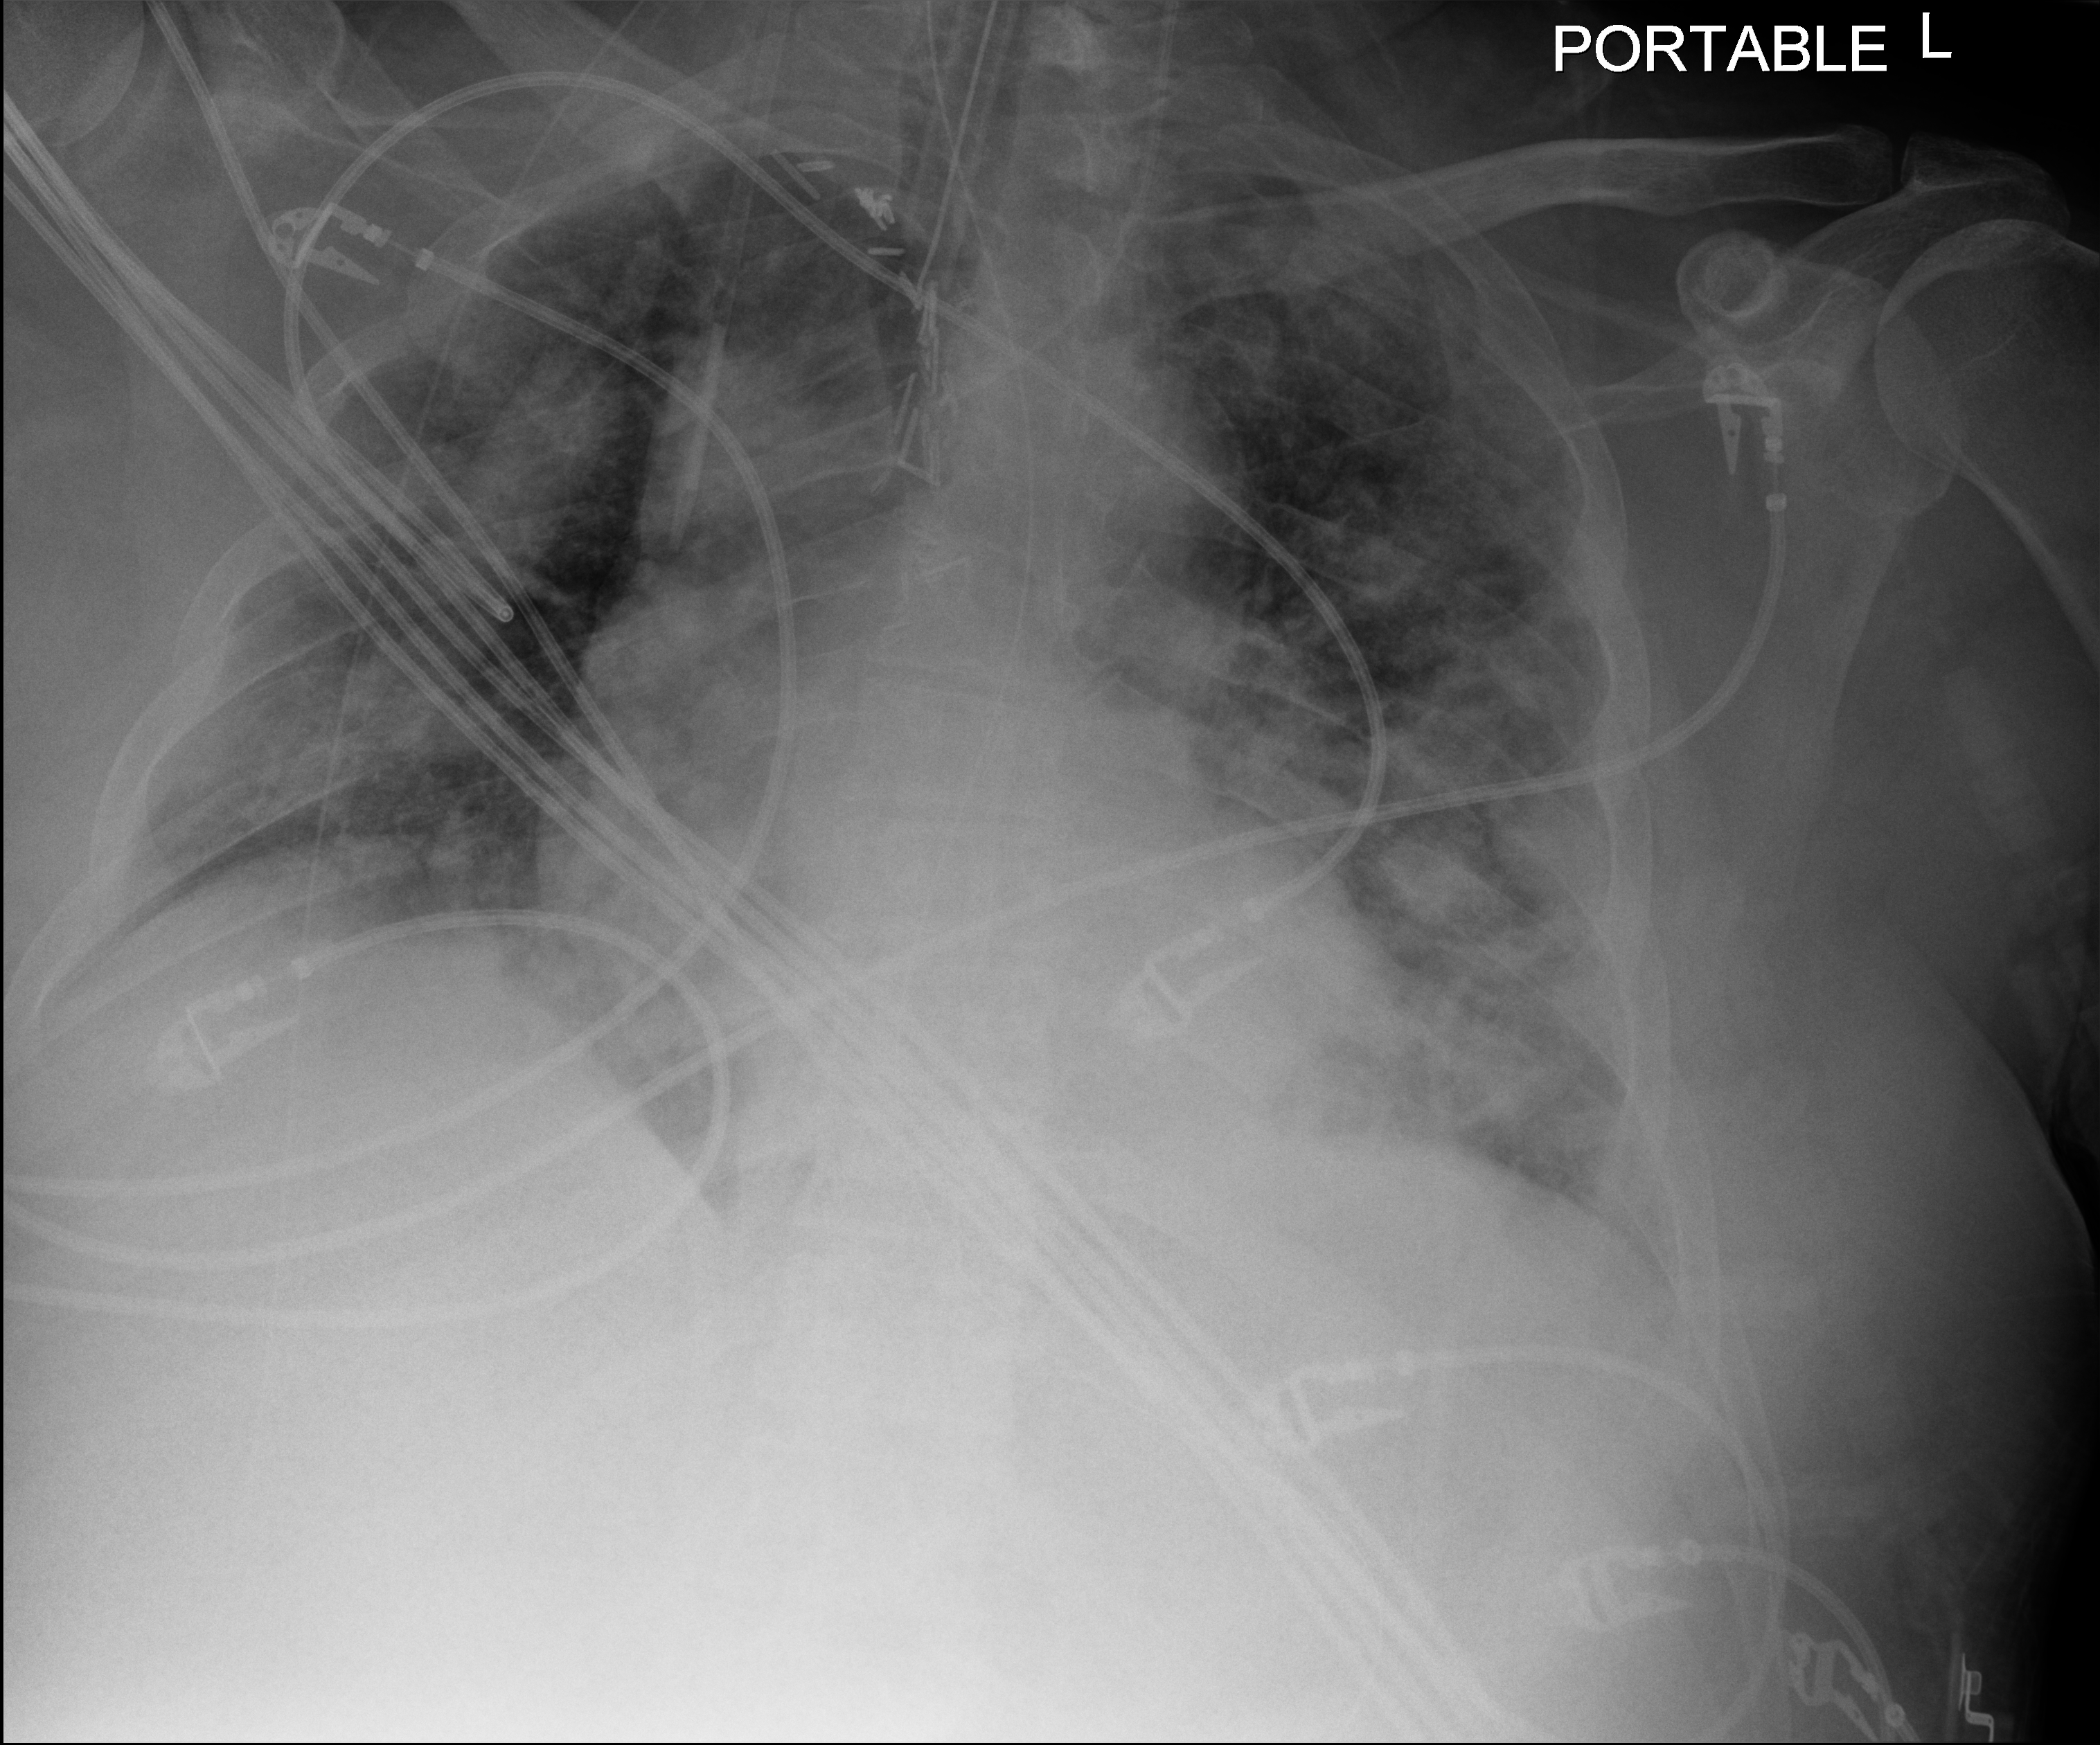
Portable chest radiograph; anteroposterior (AP) projection. Adult patient hospitalised with COVID-19, age 18–59 years.
Hospital-stay facts (about this admission, not read from this image; timing relative to this image not recorded): admitted to intensive care during this hospital stay: yes.